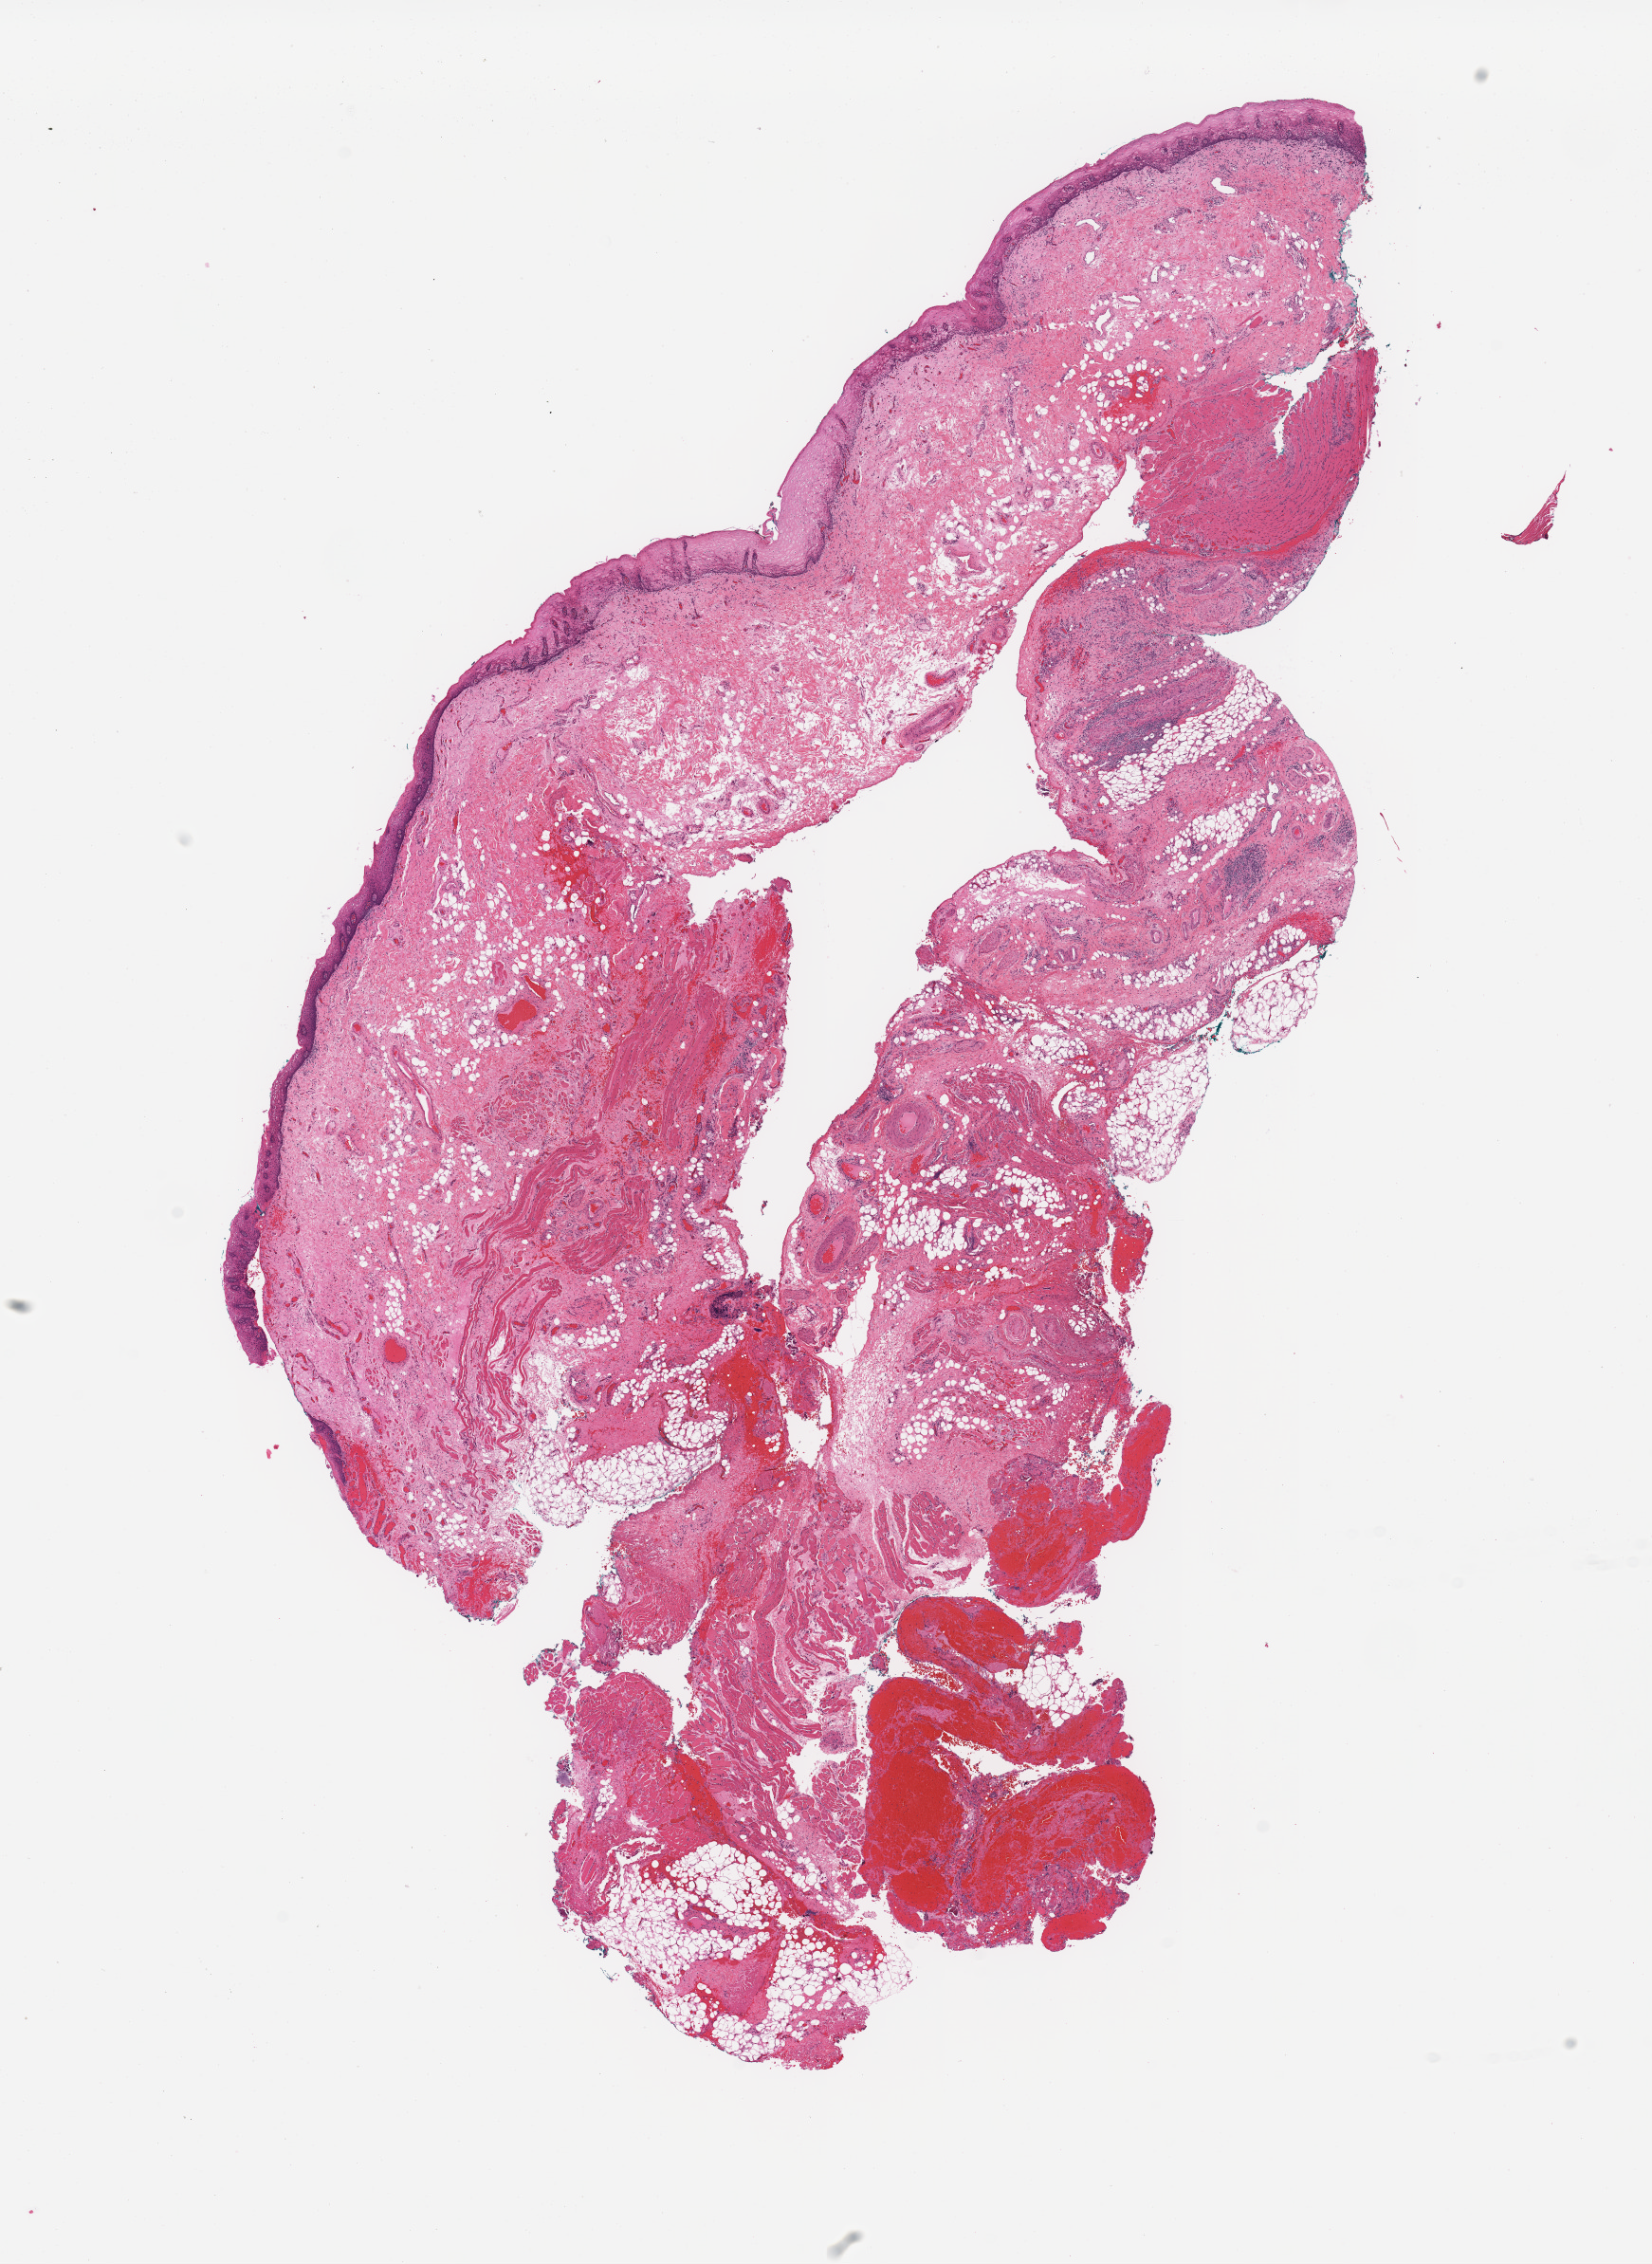
Whole-slide histology image, Hematoxylin and eosin (H&E) stained — whole scanned area (about 13.8 x 18.9 mm) shown as a low-resolution overview, head and neck, tissue type not recorded. Male, 56 y/o.
Patient diagnosis: Squamous cell carcinoma, NOS (cheek mucosa).